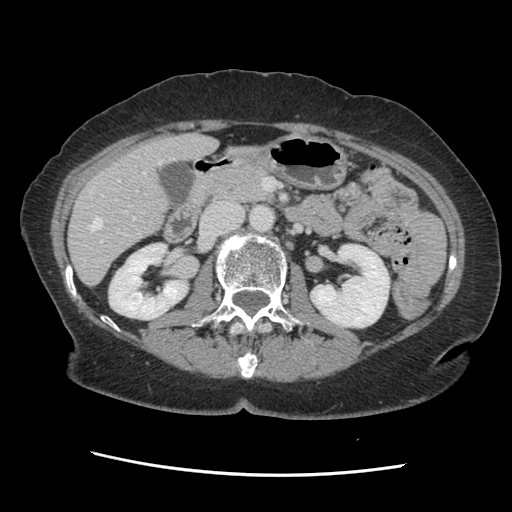
Contrast-enhanced abdominal CT, one axial slice; slice 63 of 141 in the series (ordered by position); 120 kVp; soft-tissue window (W 400 / L 40 HU); 2.5 mm slice thickness; 512 × 512 image matrix. Female patient, age 61 years. Case-level facts recorded for this patient, not image findings: diagnosis: colorectal cancer liver metastases, imaged before liver resection; multiple liver metastases: no; largest metastasis: 2.4 cm; chemotherapy before resection: no.
Outlined on this slice (expert manual segmentation):
- hepatic veins: bounding box (x1, y1, x2, y2) in pixels: (87, 160, 162, 231)
- liver: (70, 135, 243, 284)
- planned liver remnant (the part of the liver to remain after resection): (70, 136, 243, 284)
- portal vein (with intrahepatic branches): (100, 180, 138, 243)